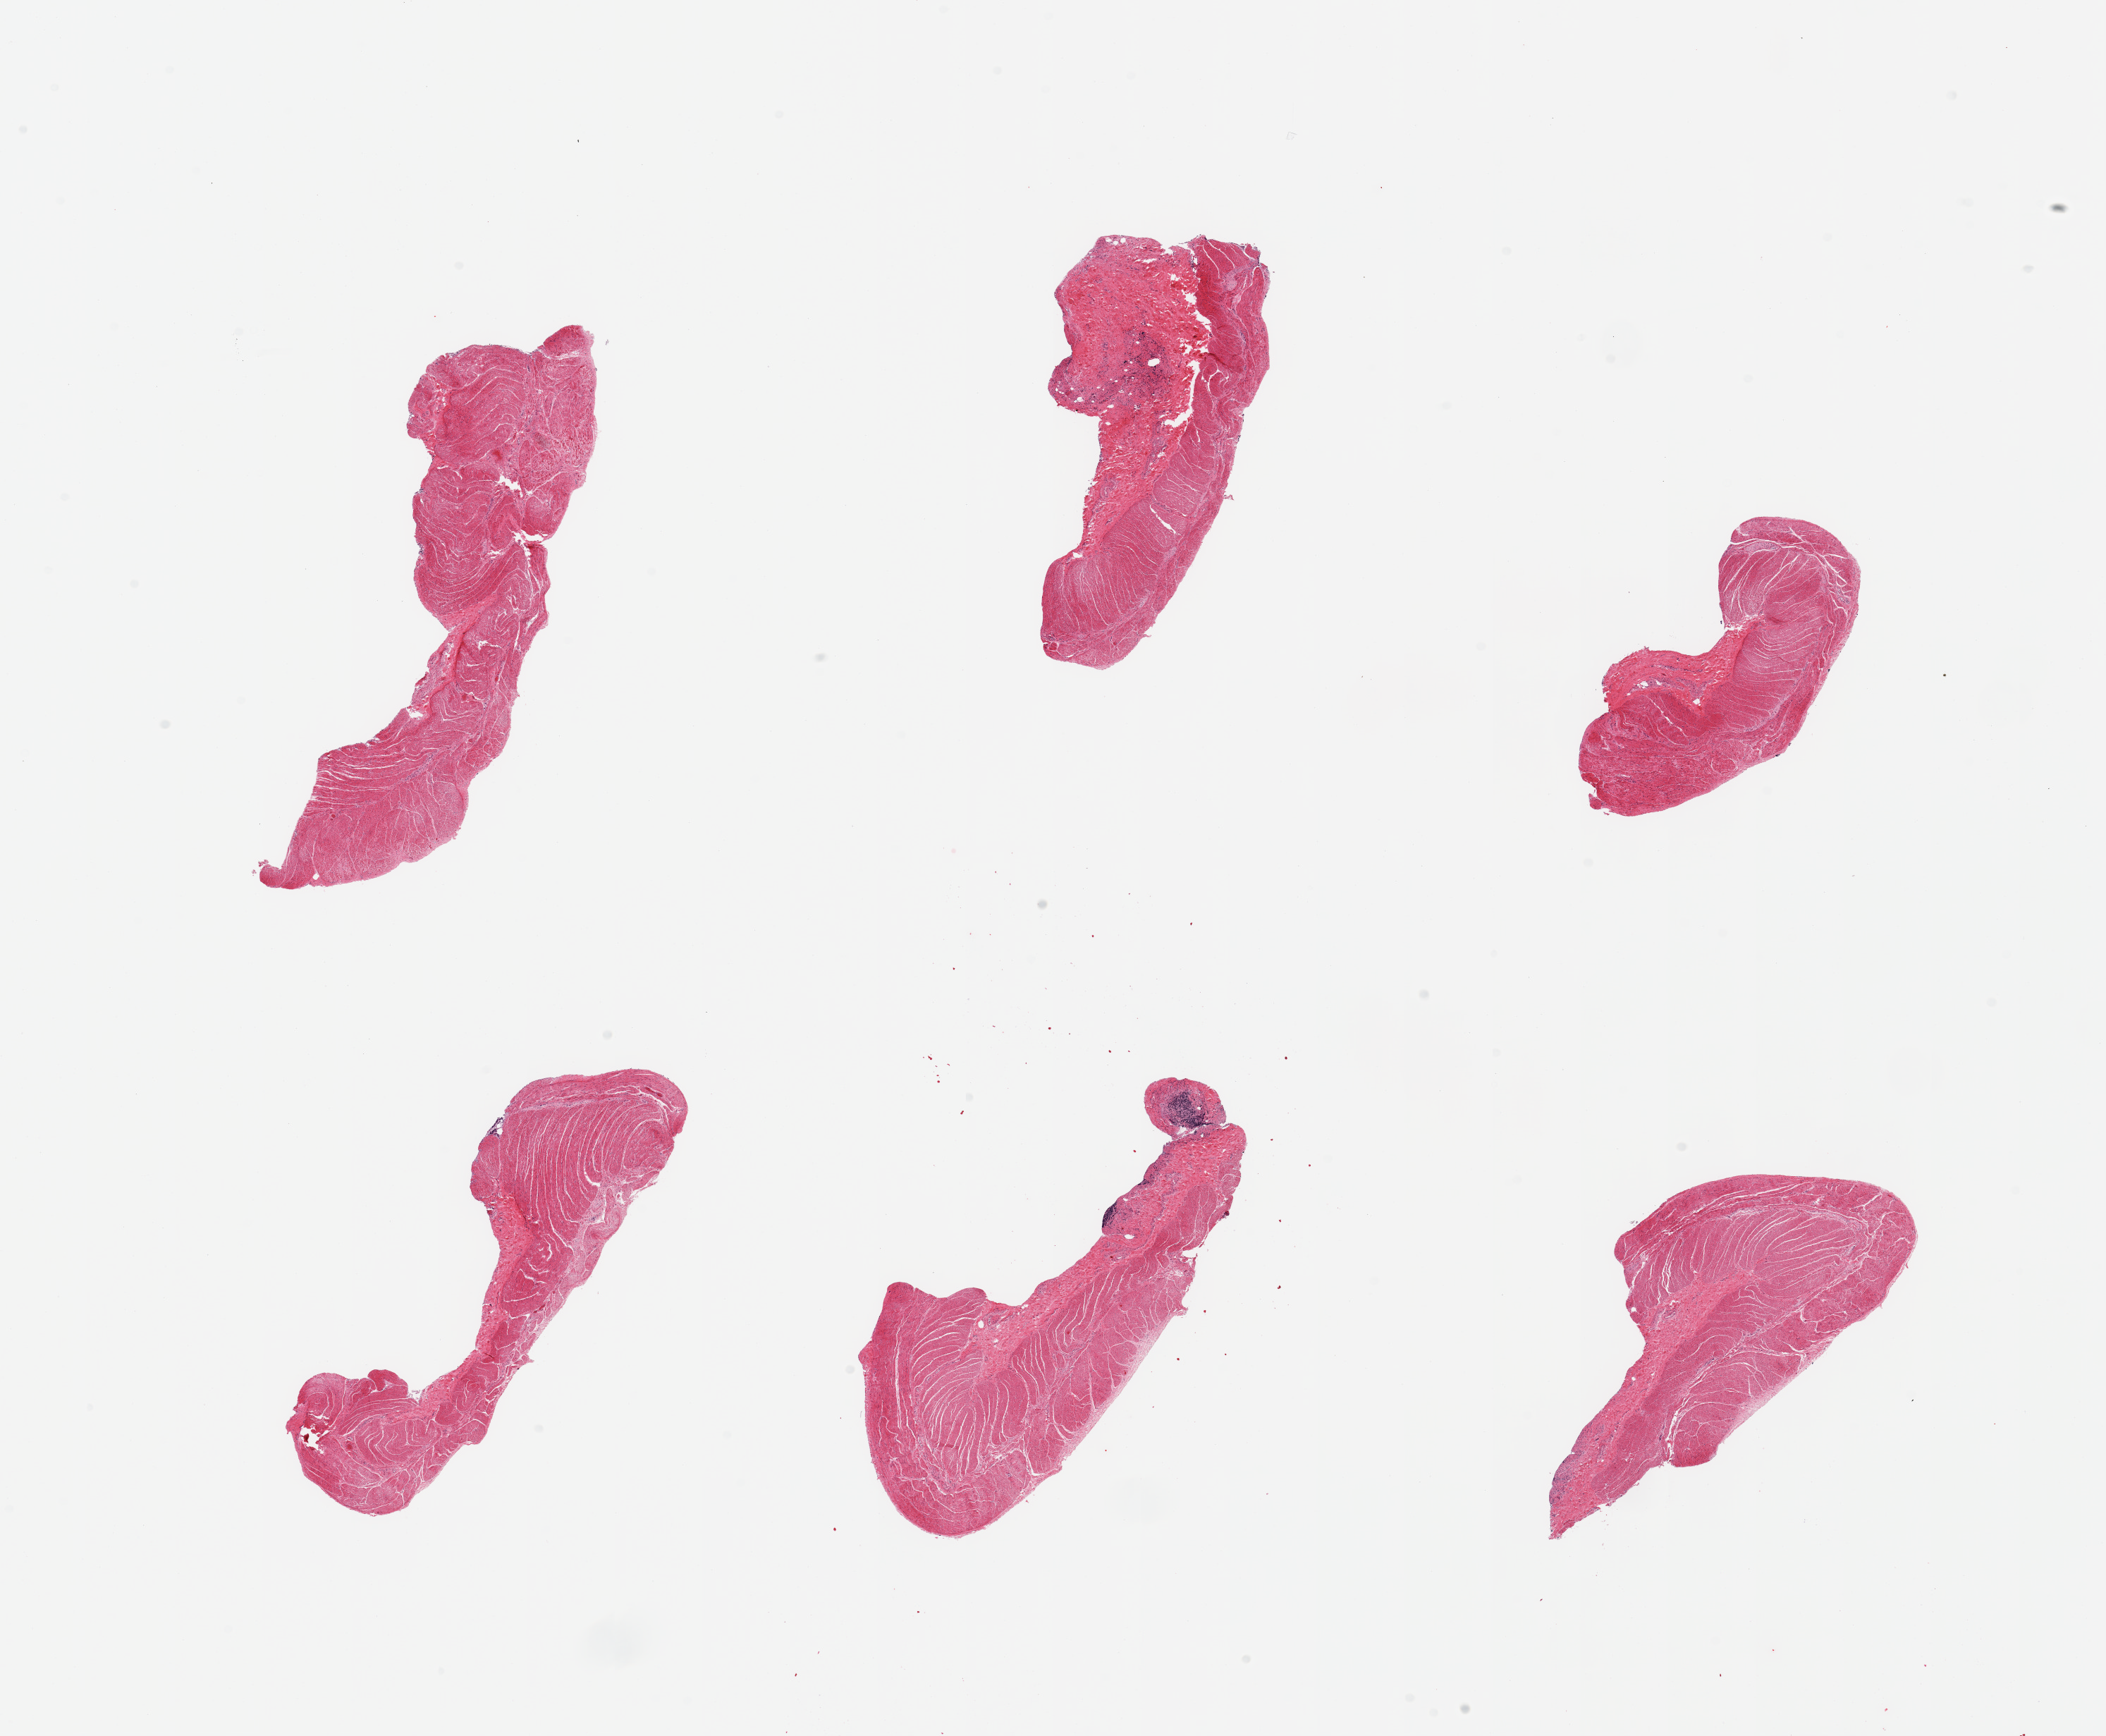
Digitized H&E-stained section, brightfield, a low-resolution overview of the entire scanned area, about 23.6 x 19.5 mm. PAXgene-fixed paraffin-embedded (PFPE) section. Sampled site (target tissue): sigmoid colon. Donor tissue sample. Male donor.
- reviewer comment on this tissue sample: 6 pieces, confirmed target muscularis